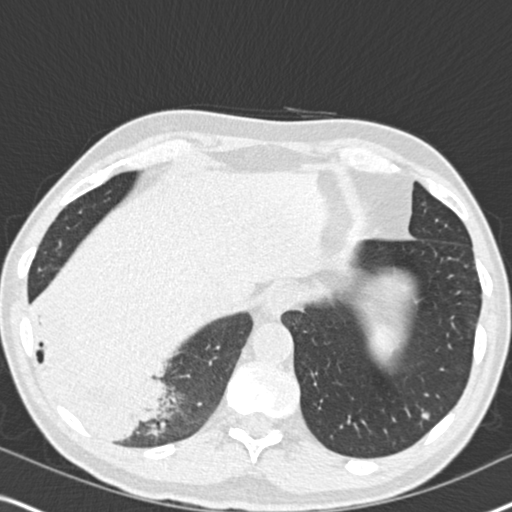
Low-dose screening chest CT, one axial slice. Slice 51 of 182 in the series (ordered by position). 120 kVp. Lung window (W 1500 / L -600 HU). 2 mm slice thickness. 512 × 512 image matrix, field of view 330 × 330 mm.
Annotated regions visible in this slice (expert manual segmentation):
- lesion 1 (tumor, lower lobe of right lung): bounding box <51,369,157,434> (left, top, right, bottom; pixels)